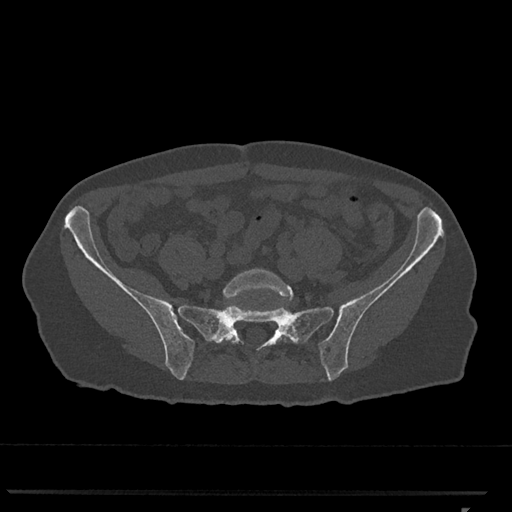
CT including the spine, one axial slice; position 117 of 793 along the scan axis; reconstruction kernel Br40s/3; 120 kVp; bone window (W 1800 / L 400 HU); 0.5 mm slice thickness; 512 × 512 image matrix, field of view 380 × 380 mm. Patient: female, 62 years. Case-level facts recorded for this patient, not image findings: primary cancer: renal.
Outlined on this slice (semi-automatically segmented with operator editing):
- L5 vertebra: bounding box (x1, y1, x2, y2) in pixels: (223, 269, 295, 342)